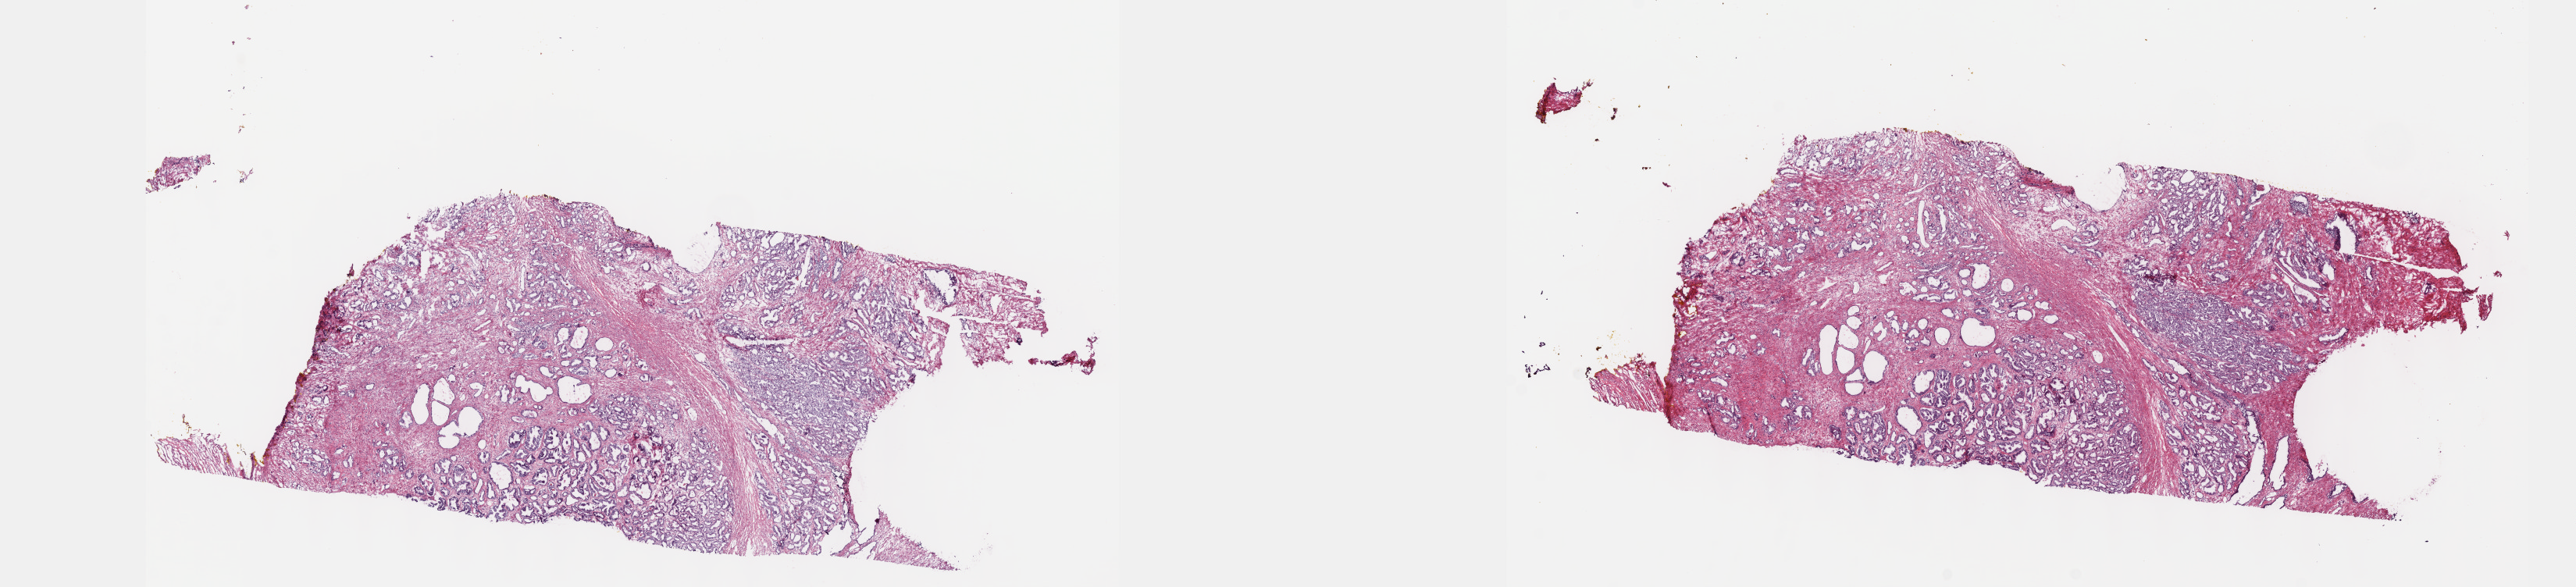
Digitized H&E tissue section (whole slide) — a low-resolution overview of the entire scanned area, about 26.7 x 6.1 mm (slide scanned at 40x); frozen section from the top of the tissue portion; sample: primary tumour, prostate. Male patient; age at initial diagnosis 62 years. Gleason score: 7 (3+4). Composition of this section per pathologist review: tumour cells 60%, tumour nuclei 60%, normal cells 0%, stromal cells 40%, necrosis 0%. Infiltration values recorded for this section: lymphocyte infiltration 40%, monocyte infiltration 20%, neutrophil infiltration 20%.
Pathologic diagnosis: Adenocarcinoma, NOS (prostate gland). Lymph nodes positive (case pathology): 0 of 2 examined. Laterality: bilateral.